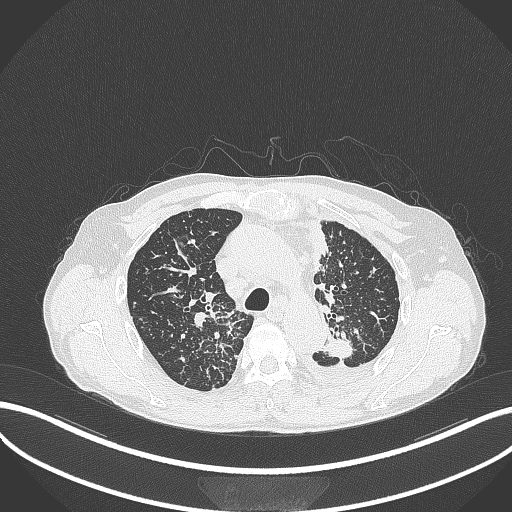
Chest CT, one axial slice; slice 257 of 325 in the series (ordered by position); lung window (W 1500 / L -600 HU); 1 mm slice thickness; 512 × 512 image matrix, field of view 400 × 400 mm. Male patient, age 58 years. Case-level facts recorded for this patient, not image findings: clinical TNM (as recorded): T1c N3 M1.
Outlined on this slice (bounding box drawn by a radiologist):
- lung tumour (recorded histology: adenocarcinoma): bounding box <322,332,358,360> (left, top, right, bottom; pixels)